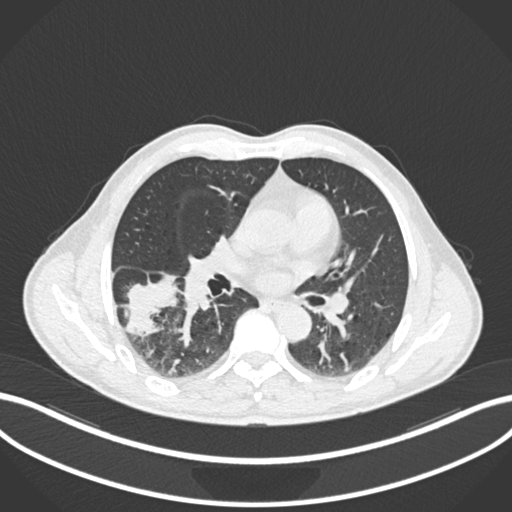
Chest CT, one axial slice; position 102 of 208 along the scan axis; lung window (W 1500 / L -600 HU); 512 × 512 image matrix, field of view 400 × 400 mm. Patient: male, 58 years. Case-level facts recorded for this patient, not image findings: clinical TNM (as recorded): T3 N0 M0; histopathological grade: G2.
Annotated regions visible in this slice (rectangle marked by the reading radiologist):
- lung tumour (recorded histology: squamous cell carcinoma): bounding box <124,266,175,338> (left, top, right, bottom; pixels)